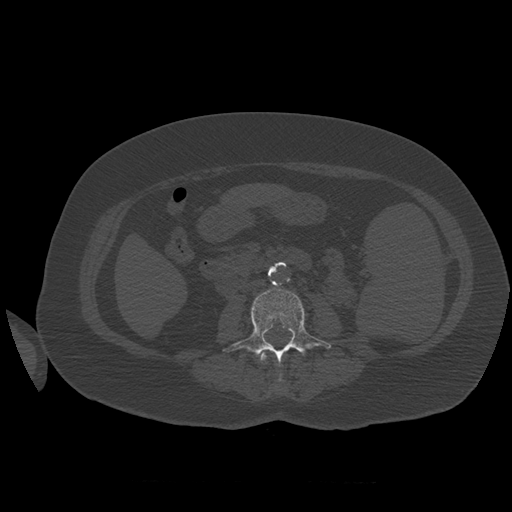
CT including the spine, one axial slice. Slice 232 of 399 in the series (ordered by position). Bone window (W 1800 / L 400 HU). 512 × 512 image matrix, field of view 404 × 404 mm. Patient age 81 years. Case-level facts recorded for this patient, not image findings: primary cancer: renal.
Annotated regions visible in this slice (semi-automatically segmented with operator editing):
- L2 vertebra: bounding box <258,352,267,361> (left, top, right, bottom; pixels)
- L3 vertebra: <224,288,331,381>